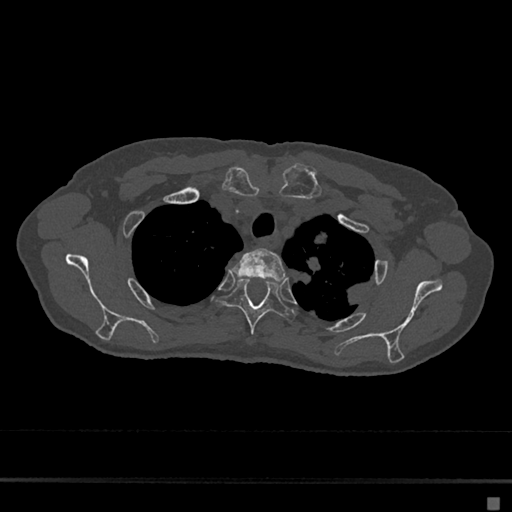
CT including the spine, one axial slice; slice 549 of 797 in the series (ordered by position); reconstruction kernel Br40s/3; 120 kVp; bone window (W 1800 / L 400 HU); 0.5 mm slice thickness; 512 × 512 image matrix, field of view 360 × 360 mm. Female patient, age 68 years. Case-level facts recorded for this patient, not image findings: primary cancer: renal.
Outlined on this slice (semi-automatically segmented with operator editing):
- T2 vertebra: bounding box [x1, y1, x2, y2] px = [232, 248, 287, 281]
- T3 vertebra: [218, 278, 295, 334]